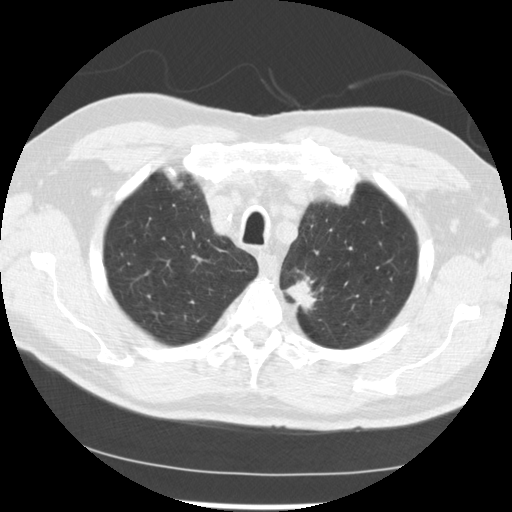
Low-dose screening chest CT, one axial slice. Position 207 of 249 along the scan axis. Reconstruction kernel STANDARD. Lung window (W 1500 / L -600 HU). 2.5 mm slice thickness. 512 × 512 image matrix, field of view 341 × 341 mm.
Structures marked on this image (manually delineated by an expert):
- lesion 2 (tumor, upper lobe of left lung): bounding box [x1, y1, x2, y2] px = [286, 280, 316, 310]